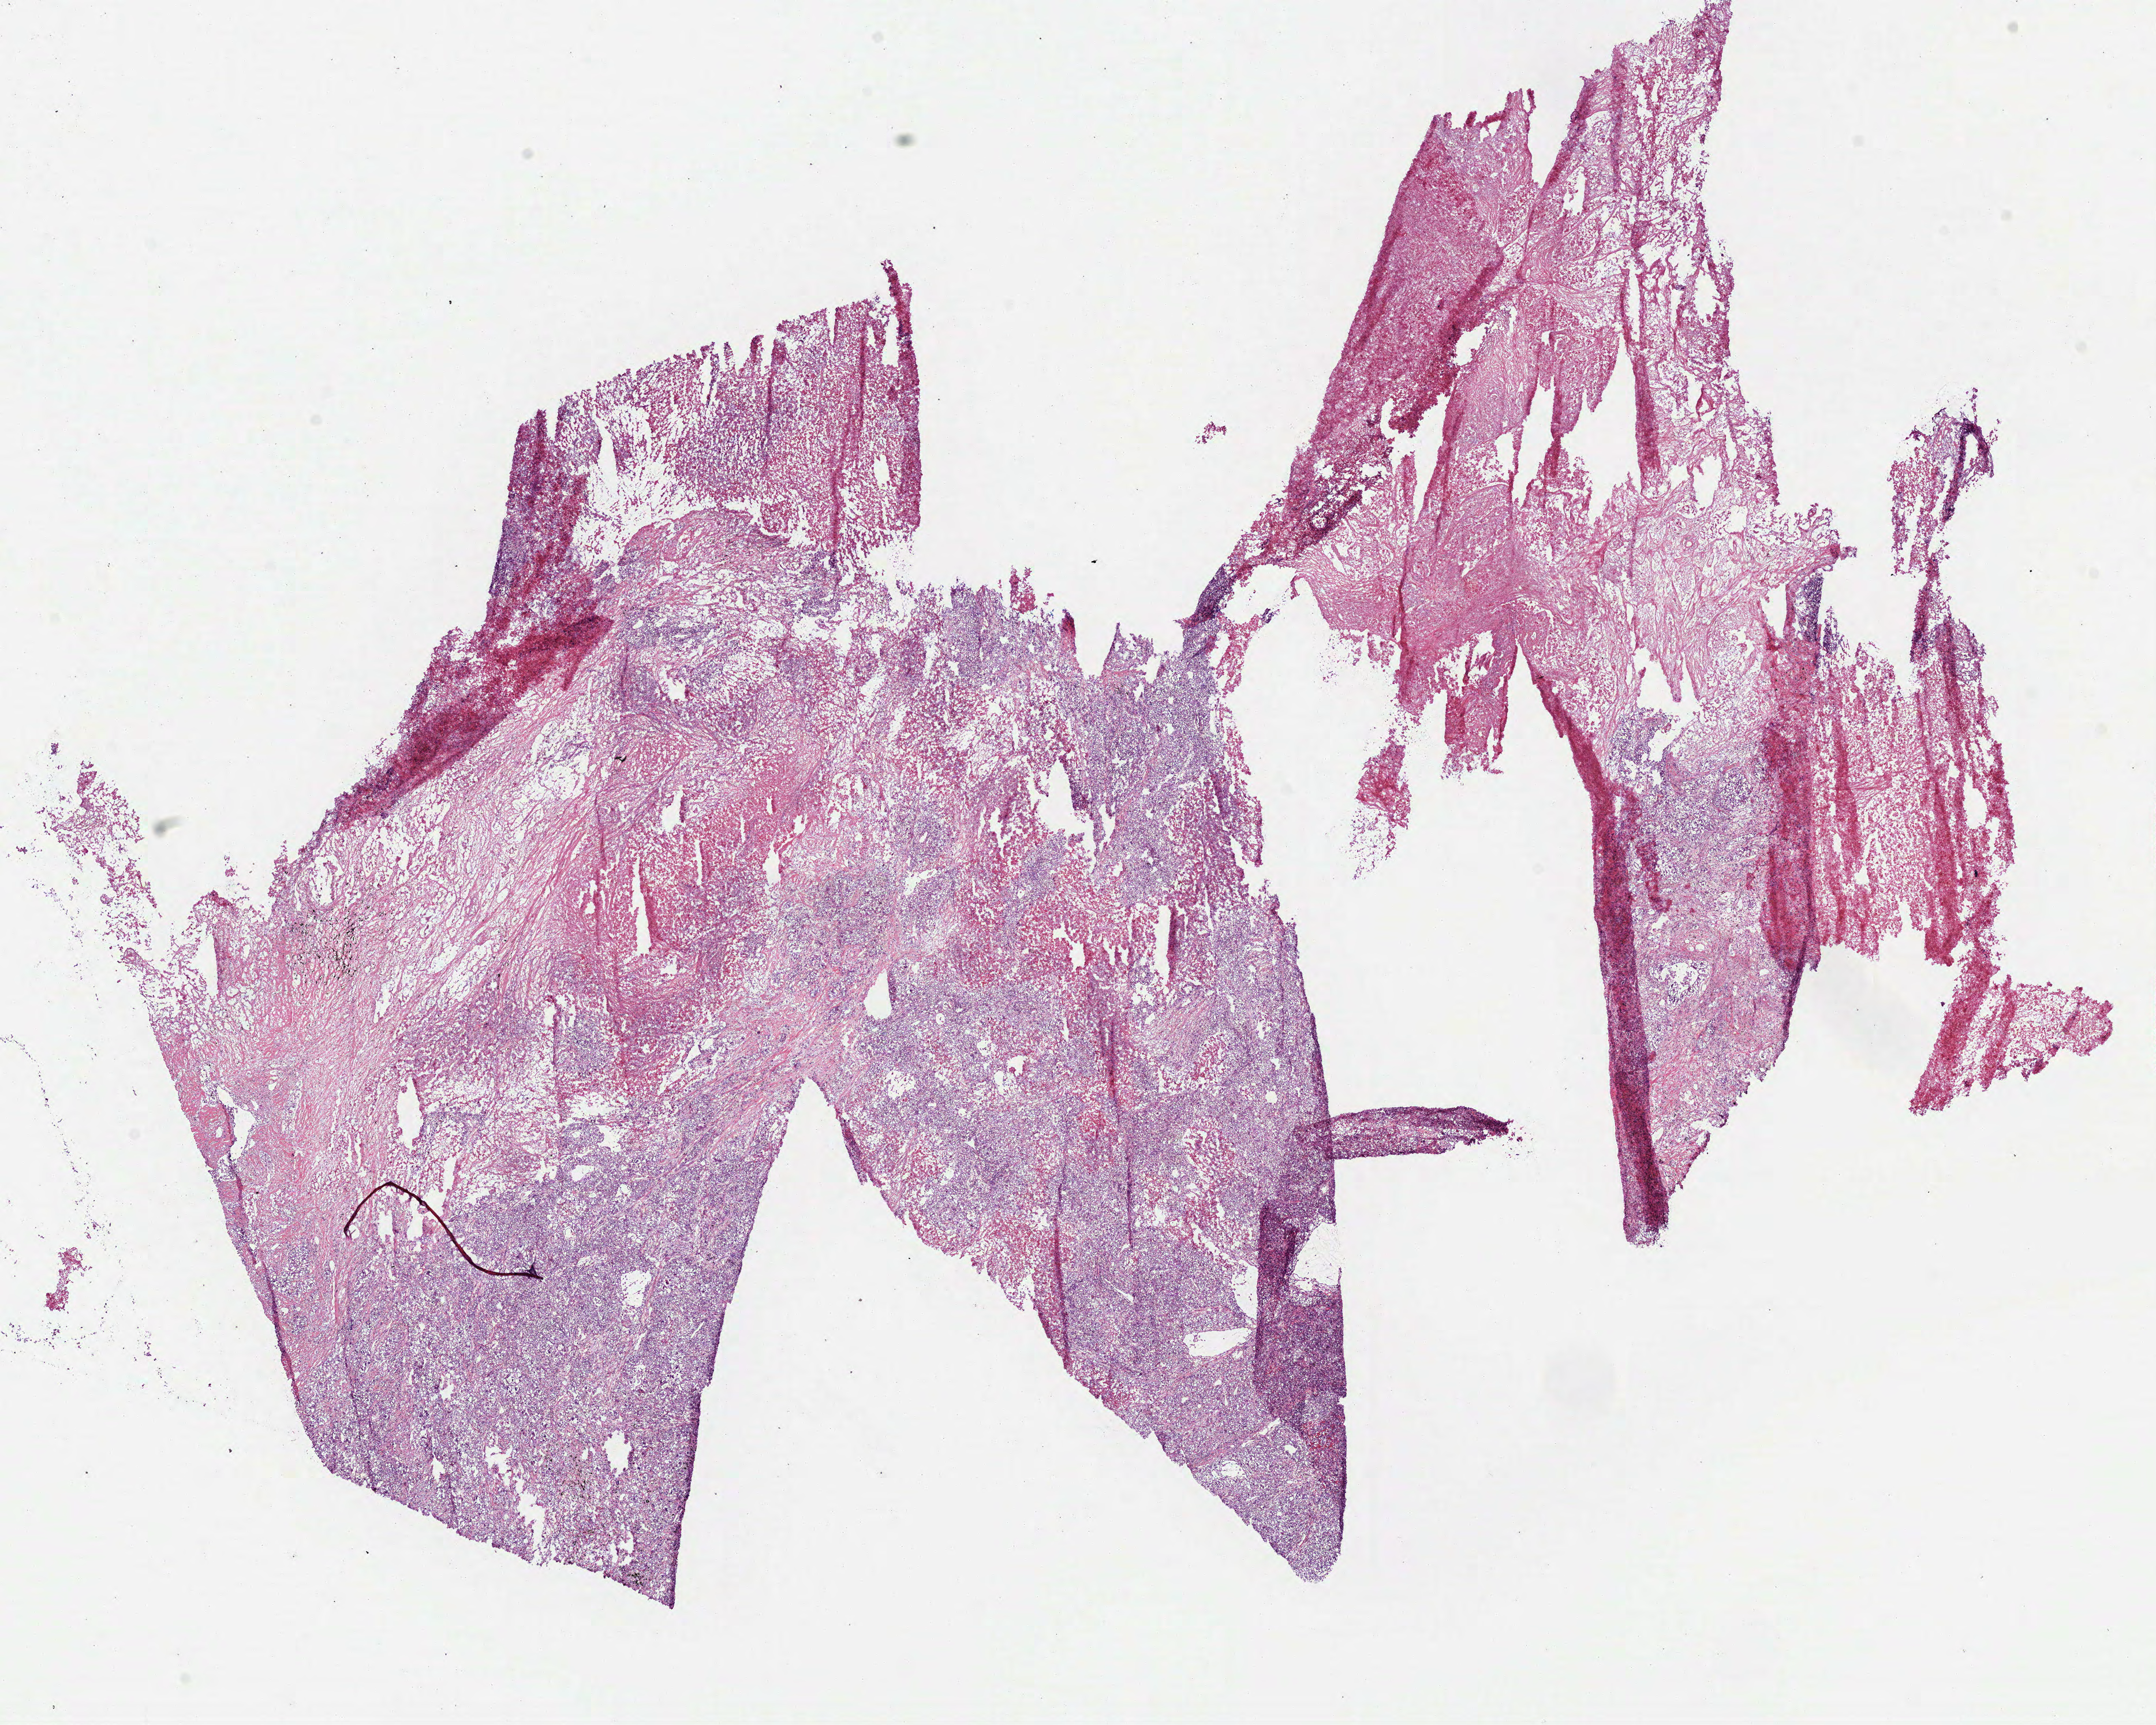
H&E whole-slide image, shown as a low-resolution overview of the whole scanned area (about 15.1 x 12.0 mm); frozen section from the bottom of the tissue portion; primary tumour sample from the lung. Female patient; age at initial diagnosis 71 years. Composition of this section per pathologist review: tumour cells 30%, tumour nuclei 80%, normal cells 0%, stromal cells 10%, necrosis 60%.
Histologic diagnosis: Adenocarcinoma, NOS (lower lobe, lung). AJCC pathologic stage: IB (6th edition). Laterality: left.